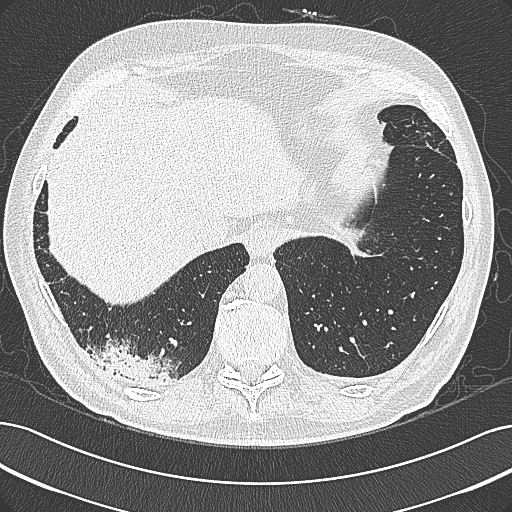
Axial slice from a low-dose chest CT screening exam, first (baseline) screen, lung window (W 1500 / L -600 HU), 1 mm slice thickness, lung (sharp) reconstruction kernel (B80f), 120 kVp, slice 241 of 355 in the series, 512 × 512 image matrix, field of view 362 × 362 mm. Male, age 68 years at enrolment. Former smoker at enrolment.
Lesion marked by an expert reader, bounding box <96,339,189,400> (left, top, right, bottom; pixels). No non-calcified nodule or mass ≥4 mm was recorded by the screening reader at this exam. Lung cancer was diagnosed 154 days after this screen: mucinous adenocarcinoma, right lower lobe, well differentiated (G1), stage IB (AJCC 6th edition), 50 mm at pathology.